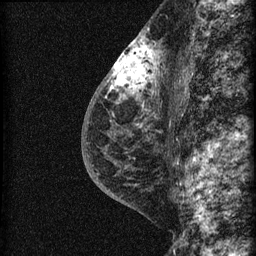
Breast MRI (dynamic contrast-enhanced), one sagittal slice; dynamic contrast-enhanced series, image 2 of 3 at this slice position (ordered by acquisition); 1.5 T; TE 4.2 ms, TR 22.7 ms; 1.5 mm slice thickness; 256 × 256 image matrix. Patient: female, 48 years. From the clinical record (not read from this slice): setting: breast cancer imaged before/during neoadjuvant chemotherapy; receptor status: triple-negative.
Outlined on this slice (semi-automatic segmentation, software-assisted and operator-edited):
- analysis volume of interest (the breast-tissue region the enhancement analysis was run in; not a lesion): bounding box [x1, y1, x2, y2] px = [115, 34, 169, 162]
- tumour enhancement mask (voxels above the 90 % enhancement threshold inside the analysis volume of interest): [115, 35, 158, 95]